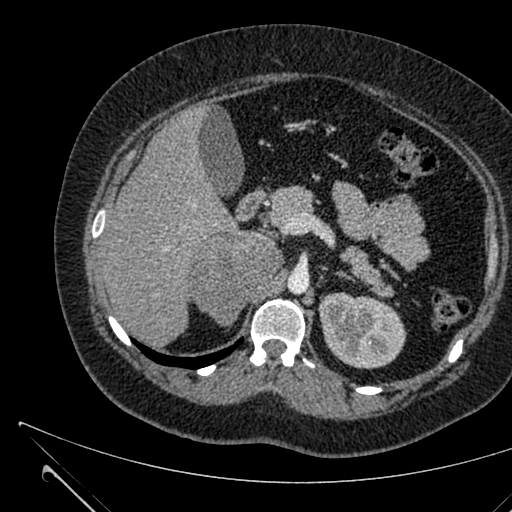
Contrast-enhanced abdominal CT, one axial slice; position 418 of 731 along the scan axis; intravenous contrast given; soft-tissue window (W 400 / L 40 HU); 1 mm slice thickness; 512 × 512 image matrix, field of view 376 × 376 mm. Female patient, age 36 years. Case-level facts recorded for this patient, not image findings: diagnosis: adrenocortical carcinoma; tumour side: right adrenal; tumour size at pathology: 10 cm; Ki-67 index: 20 %; stage (as recorded): 4.
Outlined on this slice (semi-automatically segmented with operator editing):
- mass: bounding box (x1, y1, x2, y2) in pixels: (193, 231, 279, 326)